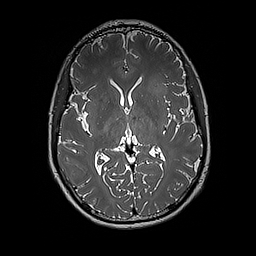
Brain MRI from a brain-tumour surgery series, one axial slice; slice 98 of 192 in the series (ordered by position); 256 × 256 image matrix, field of view 250 × 250 mm. From the clinical record (not read from this slice): histopathology: Glioblastoma; WHO grade: 4; IDH mutation: no.
Outlined on this slice (manually delineated by an expert):
- tumour: bounding box (x1, y1, x2, y2) in pixels: (140, 76, 171, 113)